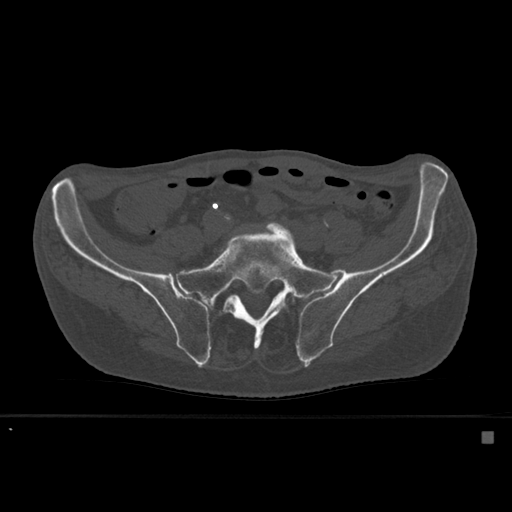
CT including the spine, one axial slice; slice 159 of 527 in the series (ordered by position); bone window (W 1800 / L 400 HU); 1.5 mm slice thickness; 512 × 512 image matrix. Male patient, age 78 years. From the clinical record (not read from this slice): primary cancer: prostate.
Annotated regions visible in this slice (semi-automatic segmentation, software-assisted and operator-edited):
- L5 vertebra: bounding box <284,298,294,308> (left, top, right, bottom; pixels)